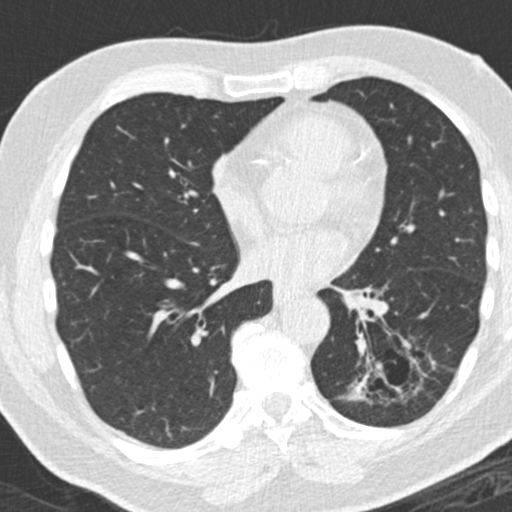
Low-dose screening chest CT, axial slice. Third annual screen. Lung window (W 1500 / L -600 HU). Slice 94 of 180 in the series. Male participant, aged 66 years at enrolment. Former smoker at enrolment.
- Expert reader's lesion annotation, bounding box (x1, y1, x2, y2) in pixels: (355, 346, 426, 428).
- Reader record for this screening exam (exam-level; its link to the box is not recorded): non-calcified nodule or mass ≥4 mm, left lower lobe, 31 × 24 mm, spiculated (stellate) margins, pre-existing on the prior screen: yes; interval growth: yes.
- Official screen result: positive, other.
- Lung cancer was diagnosed 56 days after this screen: adenocarcinoma, NOS, left lower lobe, poorly differentiated (G3), stage IB (AJCC 6th edition), 38 mm at pathology.